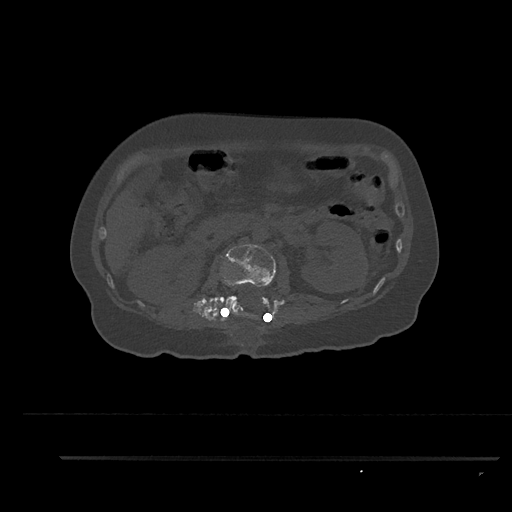
CT including the spine, one axial slice; slice 186 of 797 in the series (ordered by position); 120 kVp; bone window (W 1800 / L 400 HU); 0.5 mm slice thickness; 512 × 512 image matrix. Patient: female, 44 years. From the clinical record (not read from this slice): primary cancer: renal; vertebrae with lytic lesions (as recorded): L1.
Outlined on this slice (semi-automatic segmentation, software-assisted and operator-edited):
- L1 vertebra: bounding box [x1, y1, x2, y2] px = [231, 284, 239, 310]
- L2 vertebra: [224, 244, 275, 317]